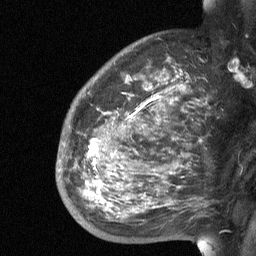
Breast MRI (dynamic contrast-enhanced), one sagittal slice. Position 46 of 64 along the scan axis. Dynamic contrast-enhanced study with each time point stored as its own series, time point 2 of 3 at this slice position (early post-contrast, ordered by acquisition time). 1.5 T. TE 4.8 ms, TR 27 ms. 256 × 256 image matrix, field of view 200 × 200 mm. Patient: female, 50 years. Case-level facts recorded for this patient, not image findings: setting: breast cancer imaged before/during neoadjuvant chemotherapy; receptor status: HER2-positive.
Structures marked on this image (semi-automatic segmentation, software-assisted and operator-edited):
- analysis volume of interest (the breast-tissue region the enhancement analysis was run in; not a lesion): bounding box [x1, y1, x2, y2] px = [56, 91, 204, 227]
- tumour enhancement mask (voxels above the 90 % enhancement threshold inside the analysis volume of interest): [88, 98, 154, 202]